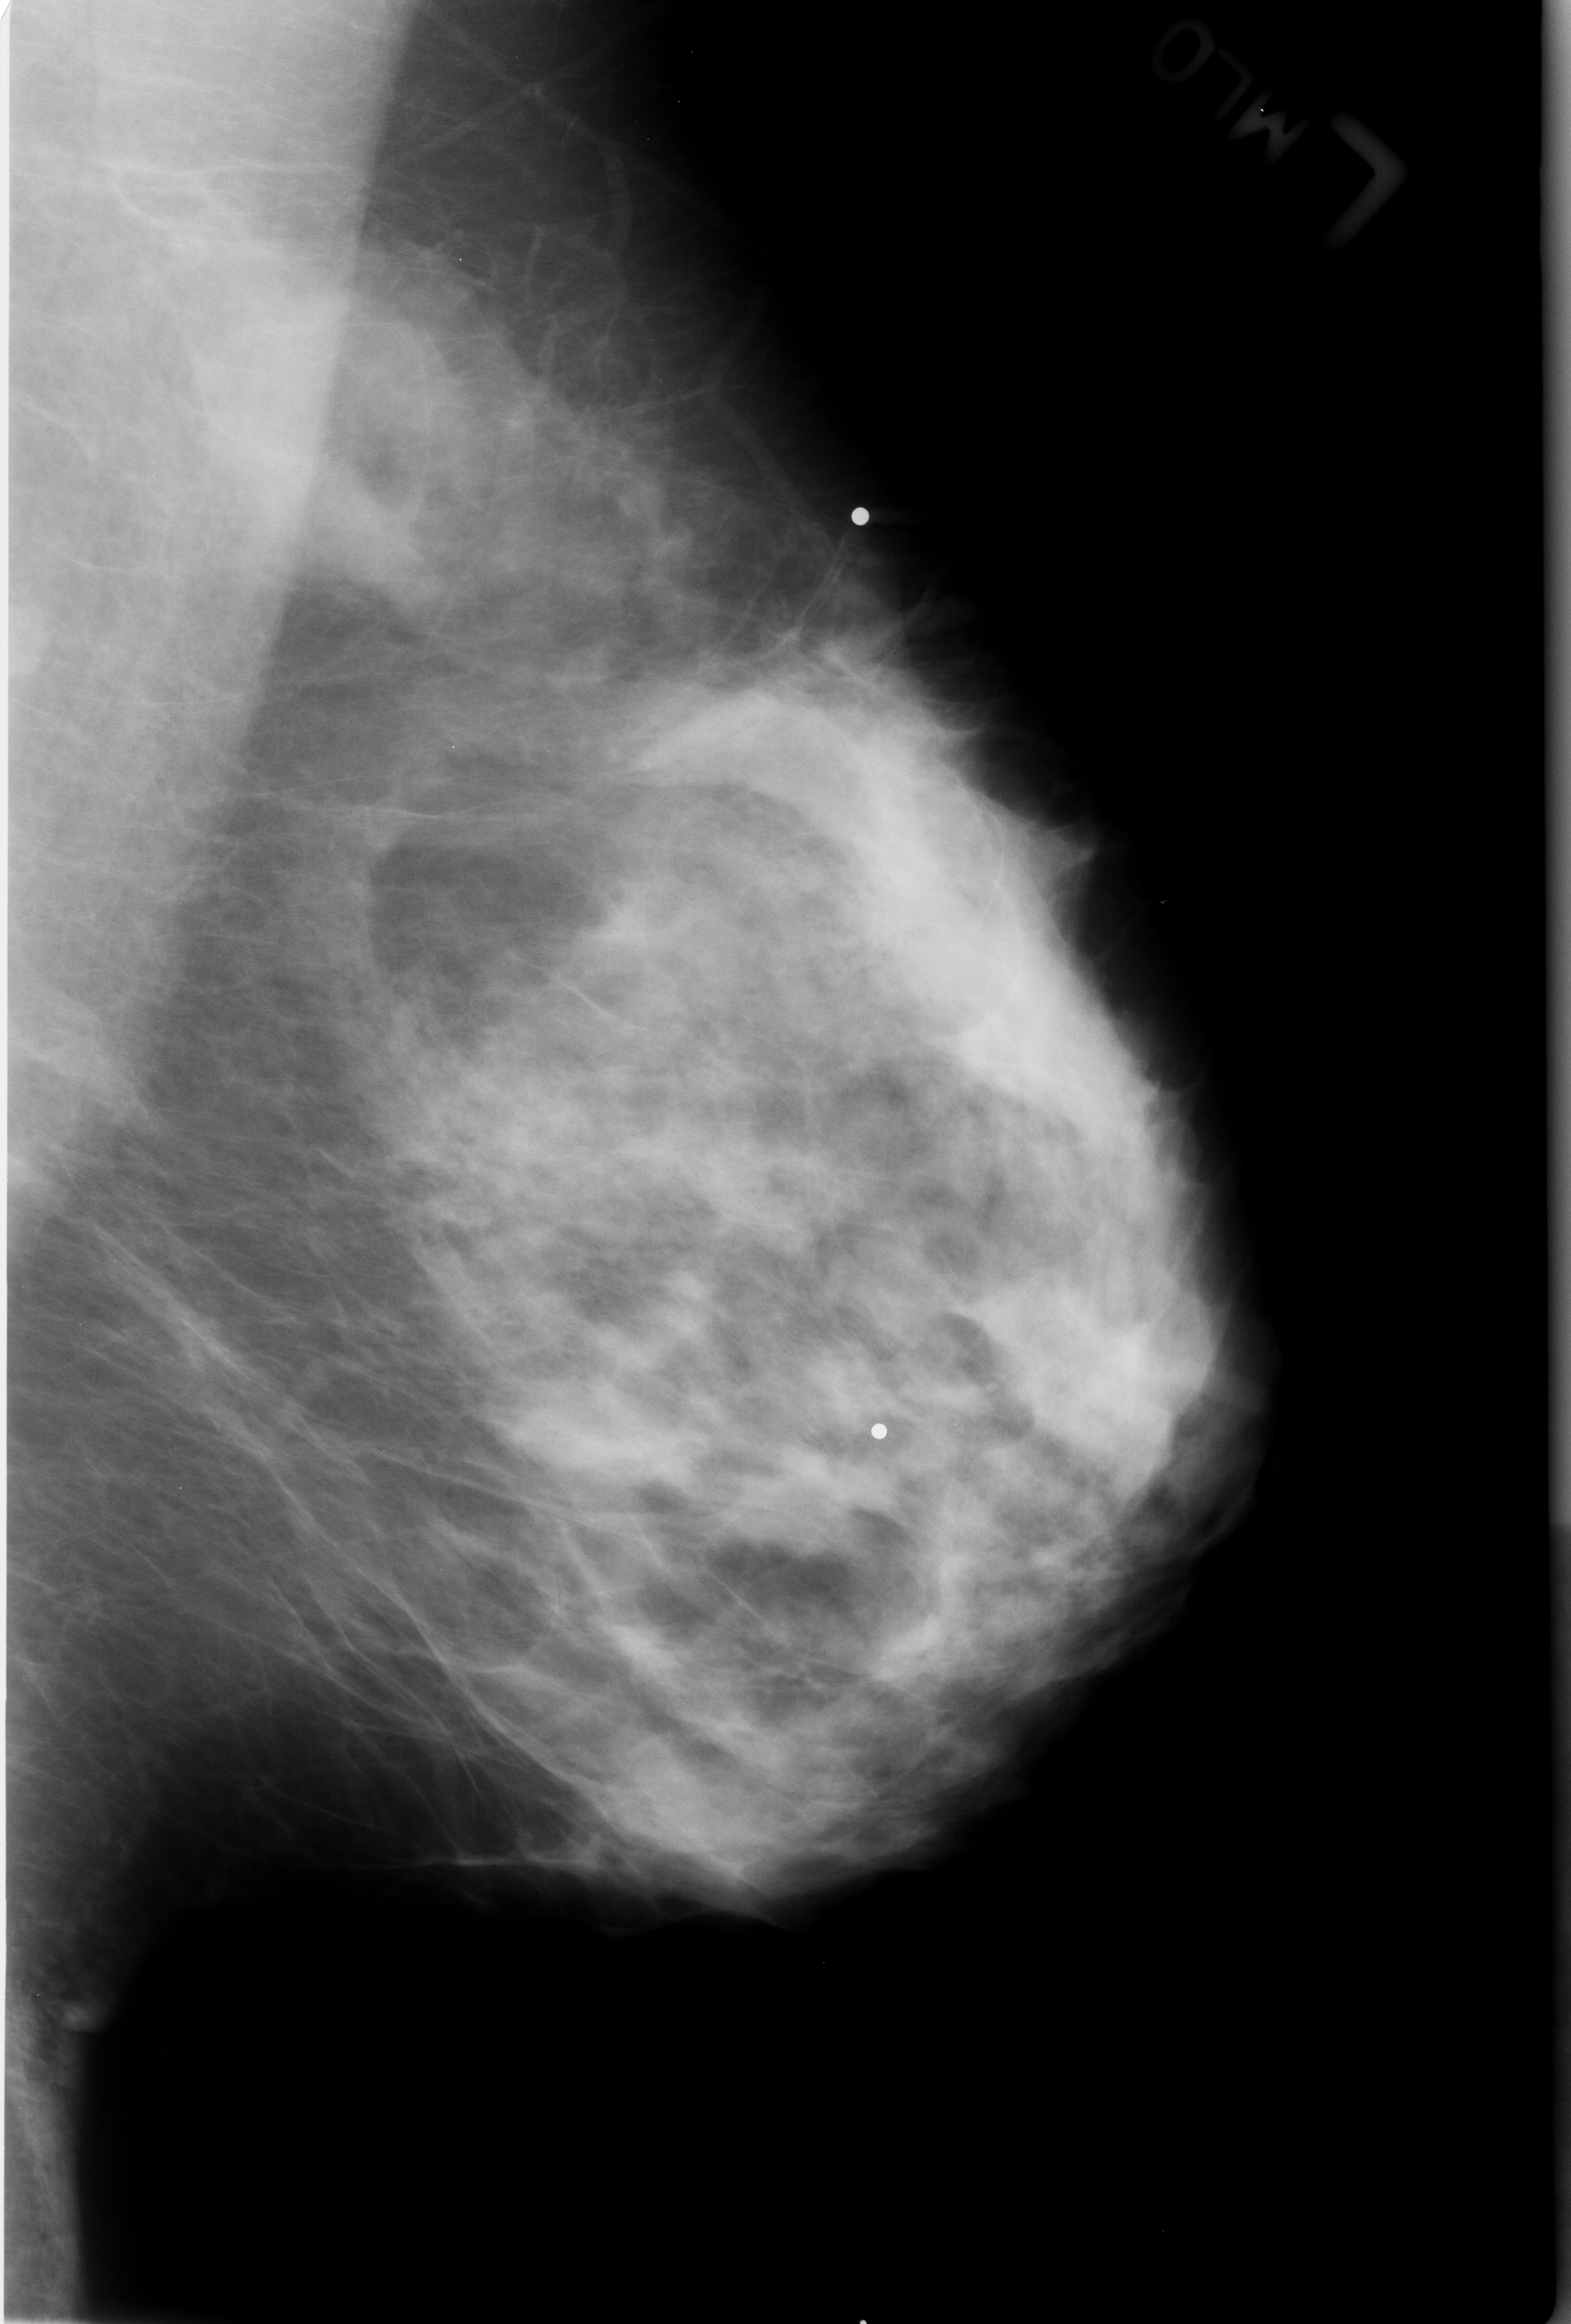
Digitized screen-film mammogram; left breast; mediolateral oblique (MLO) view; BI-RADS breast density category 3 (scale 1–4); 1571 × 2324 image matrix.
Expert-marked regions of interest on this image (one box per marked abnormality):
- mass, shape focal asymmetric density; BI-RADS assessment category 2; subtlety rating 4 on a 1 (subtle) to 5 (obvious) scale; benign; no additional work-up was recommended (outcome (as recorded, no biopsy): benign without callback): bounding box [x1, y1, x2, y2] px = [190, 256, 477, 571]